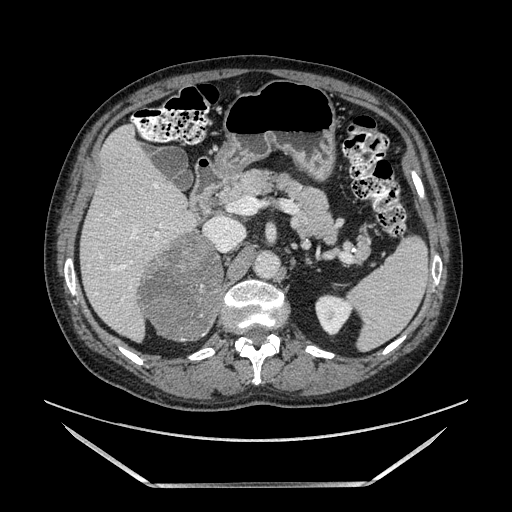
Contrast-enhanced abdominal CT, one axial slice; position 81 of 185 along the scan axis; soft-tissue window (W 400 / L 40 HU); 1.25 mm slice thickness; 512 × 512 image matrix, field of view 440 × 440 mm. Male patient. From the clinical record (not read from this slice): diagnosis: adrenocortical carcinoma; tumour side: right adrenal; tumour size at pathology: 10.3 cm; Ki-67 index: 20 %; stage (as recorded): 3.
Annotated regions visible in this slice (semi-automatically segmented with operator editing):
- mass: bounding box (x1, y1, x2, y2) in pixels: (144, 235, 221, 338)